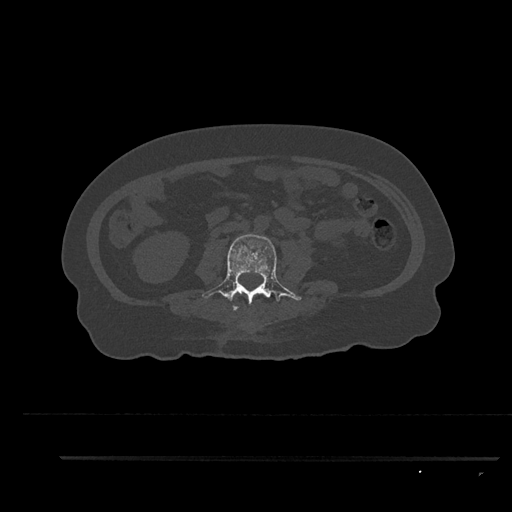
CT including the spine, one axial slice. Position 93 of 797 along the scan axis. 120 kVp. Bone window (W 1800 / L 400 HU). 0.5 mm slice thickness. 512 × 512 image matrix, field of view 408 × 408 mm. Female patient, age 44 years. Case-level facts recorded for this patient, not image findings: primary cancer: renal; vertebrae with lytic lesions (as recorded): L1.
Outlined on this slice (semi-automatic segmentation, software-assisted and operator-edited):
- L2 vertebra: bounding box <233,306,239,311> (left, top, right, bottom; pixels)
- L3 vertebra: <202,234,302,311>